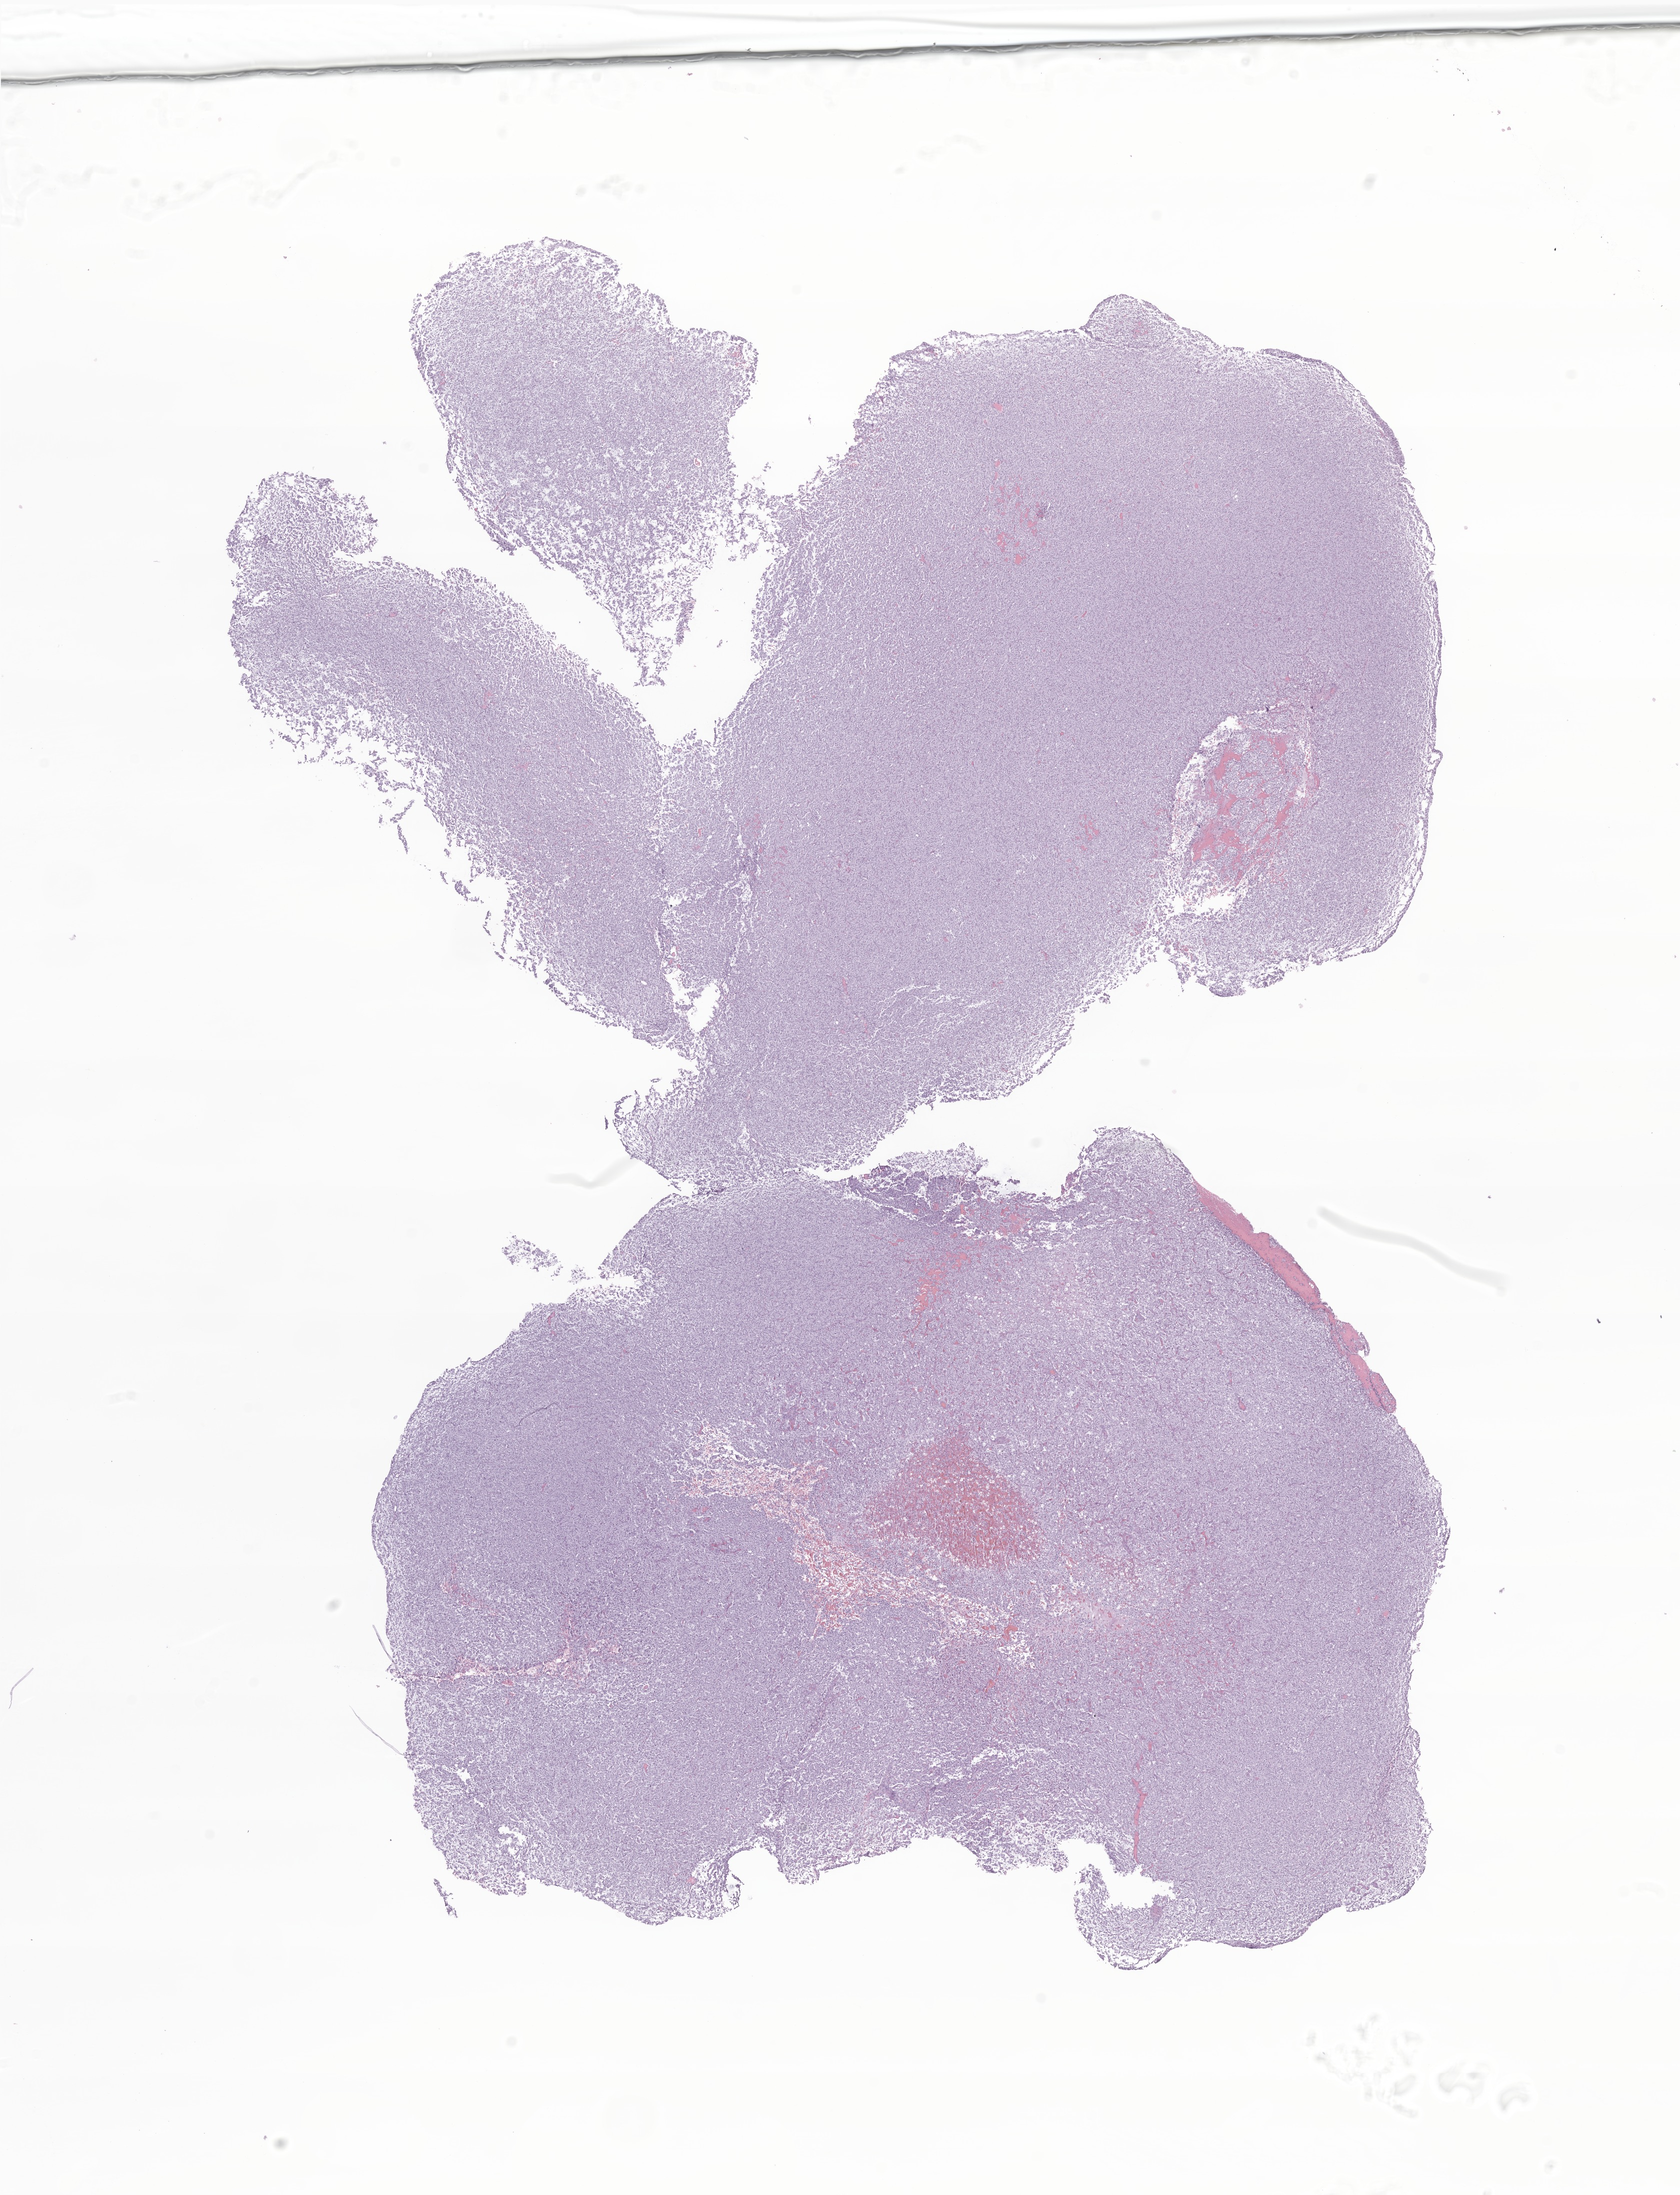
Haematoxylin and eosin whole-slide image of tumor tissue from the frontal lobe, whole scanned area (about 14.2 x 18.5 mm) shown as a low-resolution overview. Formalin-fixed, paraffin-embedded (FFPE) tissue. Male patient, age 273 months (22 years 9 months).
• diagnosis: Oligodendroglioma, NOS